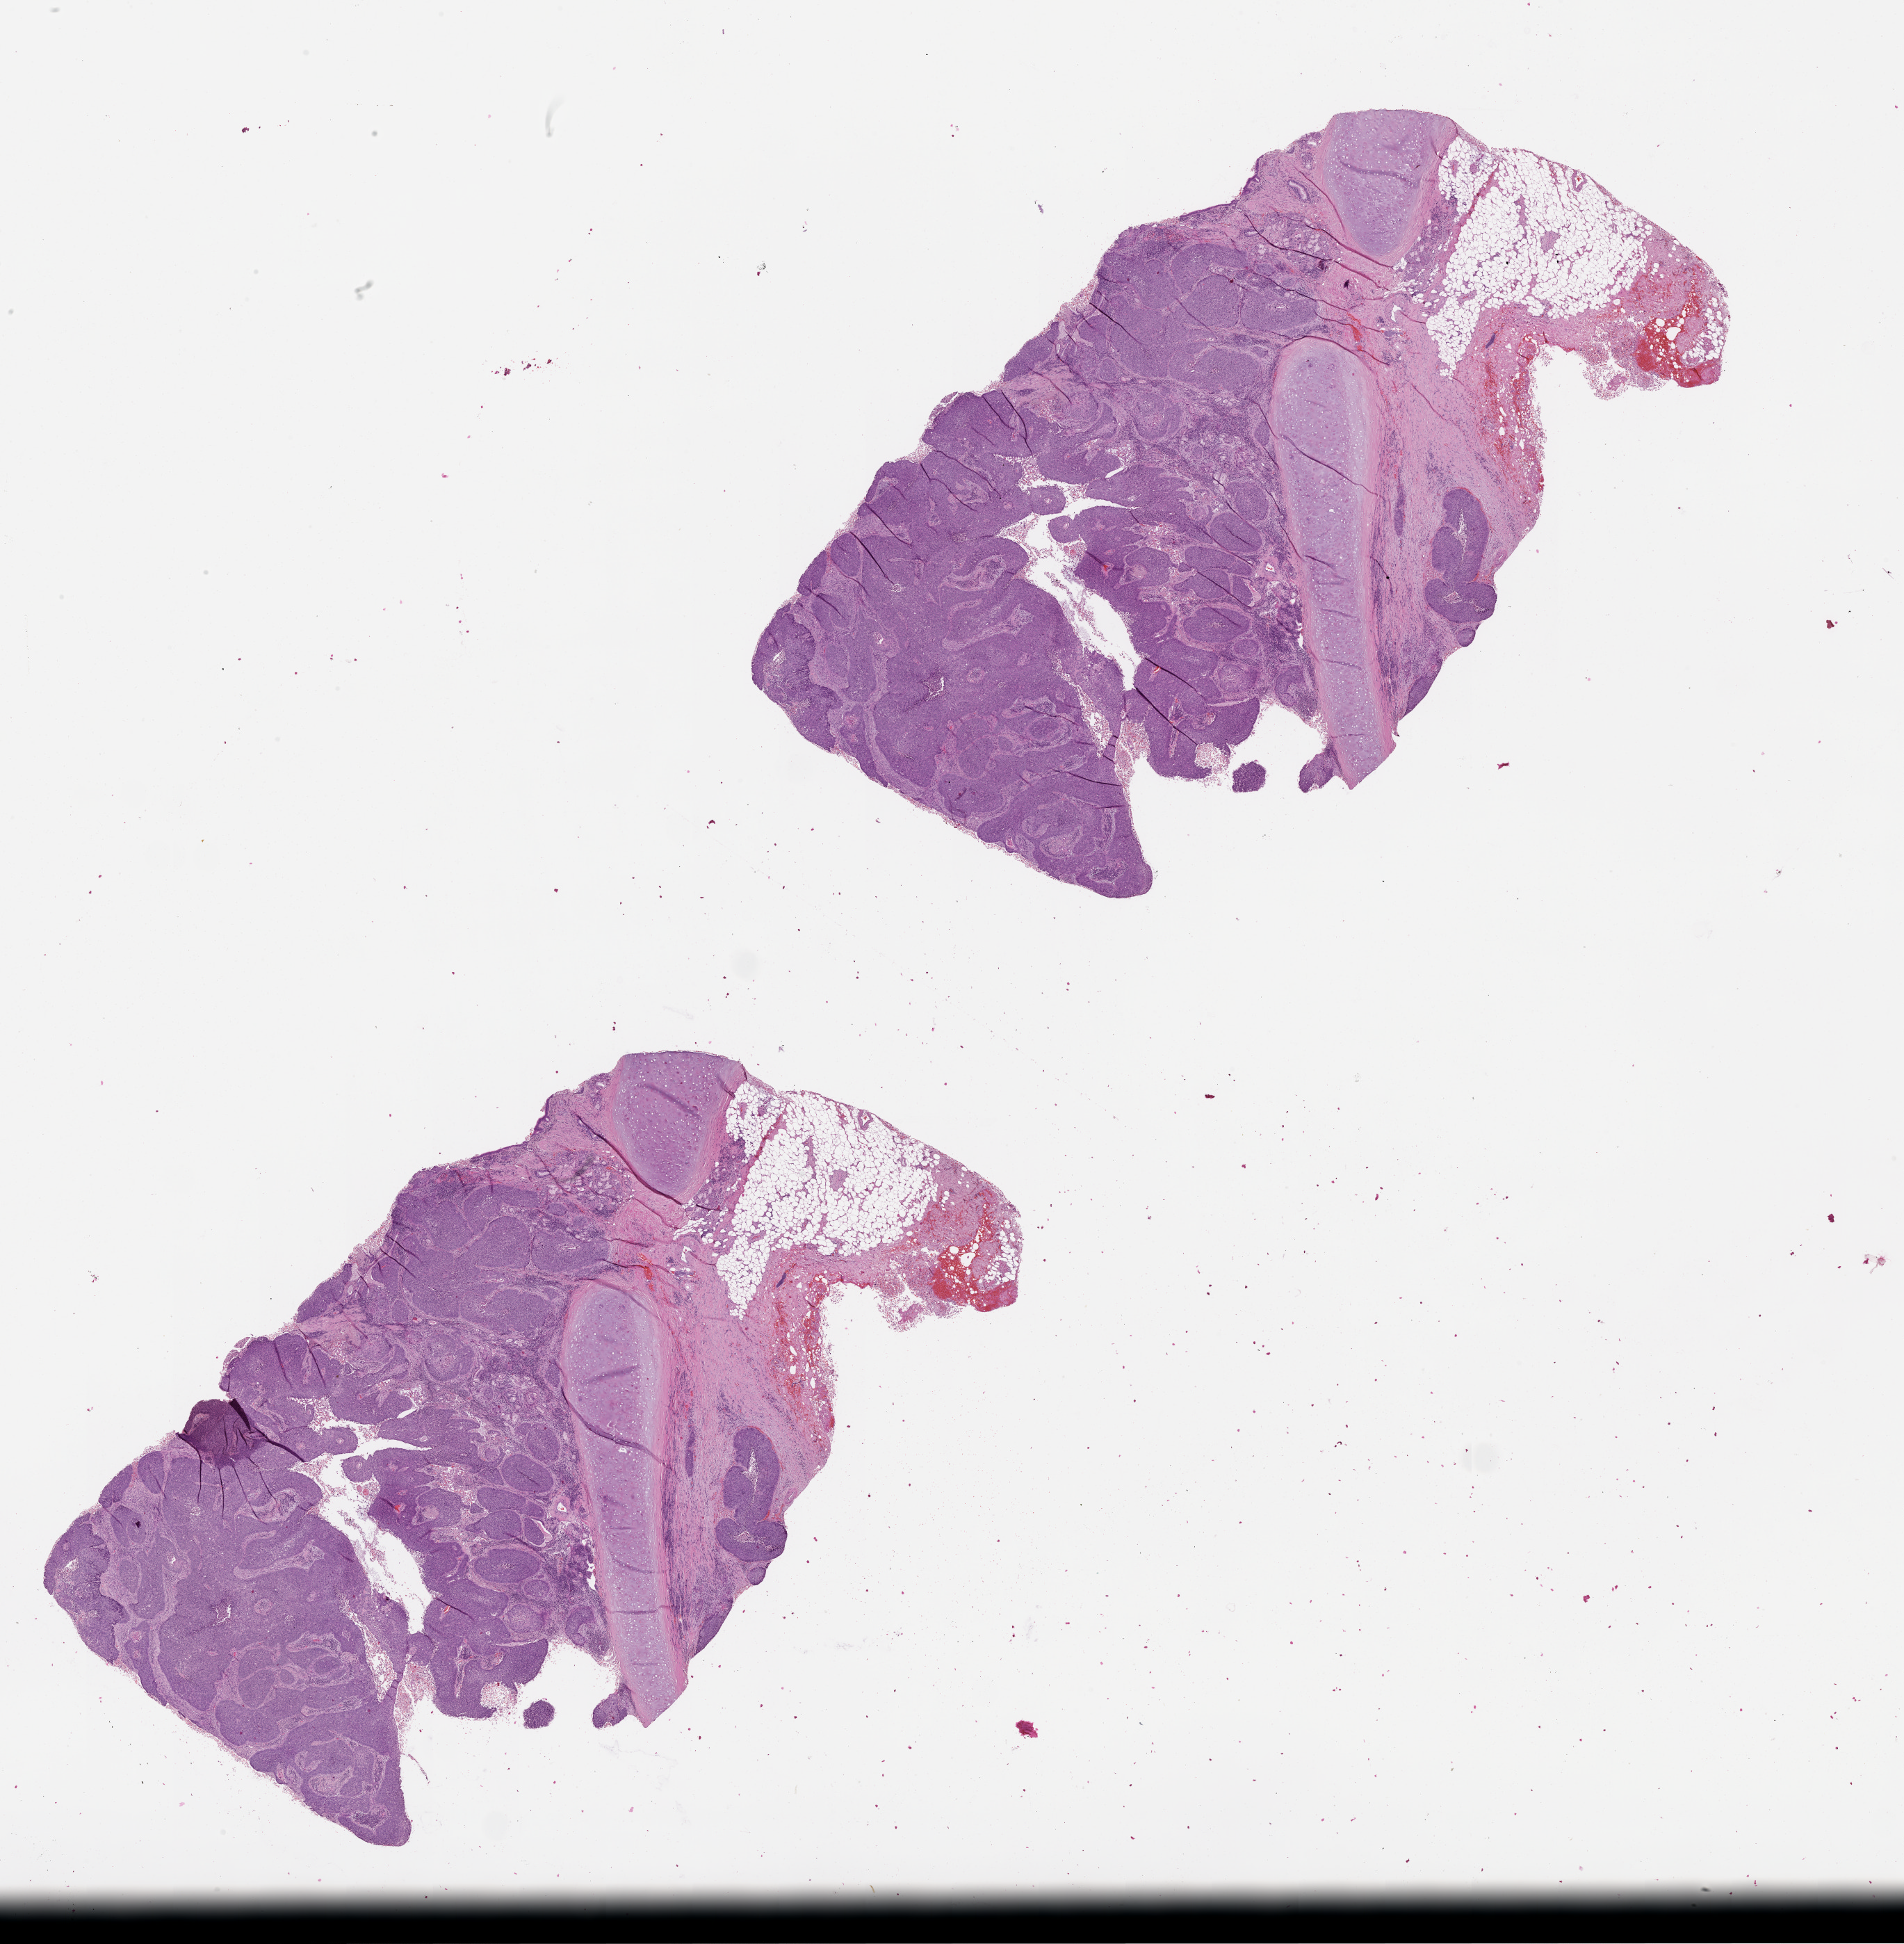
Hematoxylin and eosin (H&E) stained whole-slide image, a low-resolution overview of the entire scanned area, about 22.0 x 22.5 mm (acquisition: 20x scan); lung, tumour tissue. Male, 69 y/o.
- patient diagnosis (cohort enrolment): squamous cell carcinoma (lung)